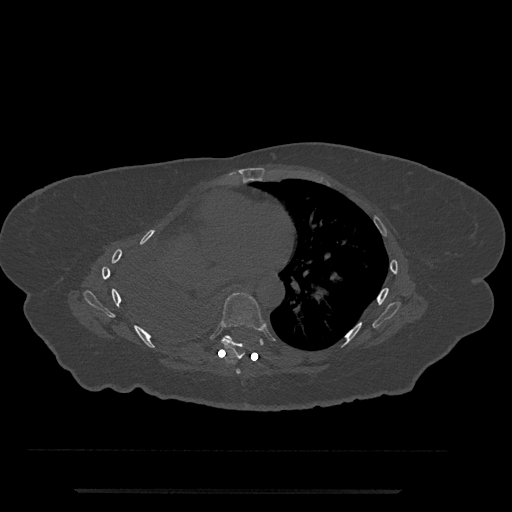
CT including the spine, one axial slice. Position 432 of 797 along the scan axis. Reconstruction kernel Br40s/3. 120 kVp. Bone window (W 1800 / L 400 HU). 0.5 mm slice thickness. 512 × 512 image matrix, field of view 440 × 440 mm. Patient: female, 51 years. From the clinical record (not read from this slice): primary cancer: neuro.
Outlined on this slice (semi-automatically segmented with operator editing):
- T6 vertebra: bounding box <236,369,241,374> (left, top, right, bottom; pixels)
- T7 vertebra: <221,293,266,359>
- T8 vertebra: <223,335,232,339>